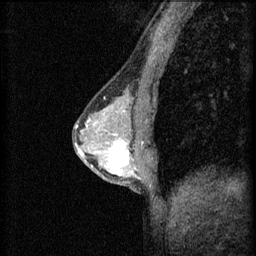
Breast MRI (dynamic contrast-enhanced), one sagittal slice; slice 29 of 60 in the series (ordered by position); 3 images stored at this slice position (order not interpretable as contrast timing); 1.5 T; TE 4.2 ms, TR 8.2 ms; 2 mm slice thickness; 256 × 256 image matrix, field of view 180 × 180 mm. Female patient, age 44 years.
Structures marked on this image (semi-automatically segmented with operator editing):
- analysis volume of interest (the breast-tissue region the enhancement analysis was run in; not a lesion): bounding box <102,132,151,181> (left, top, right, bottom; pixels)
- tumour enhancement mask (voxels above the 70 % enhancement threshold inside the analysis volume of interest): <110,140,137,177>